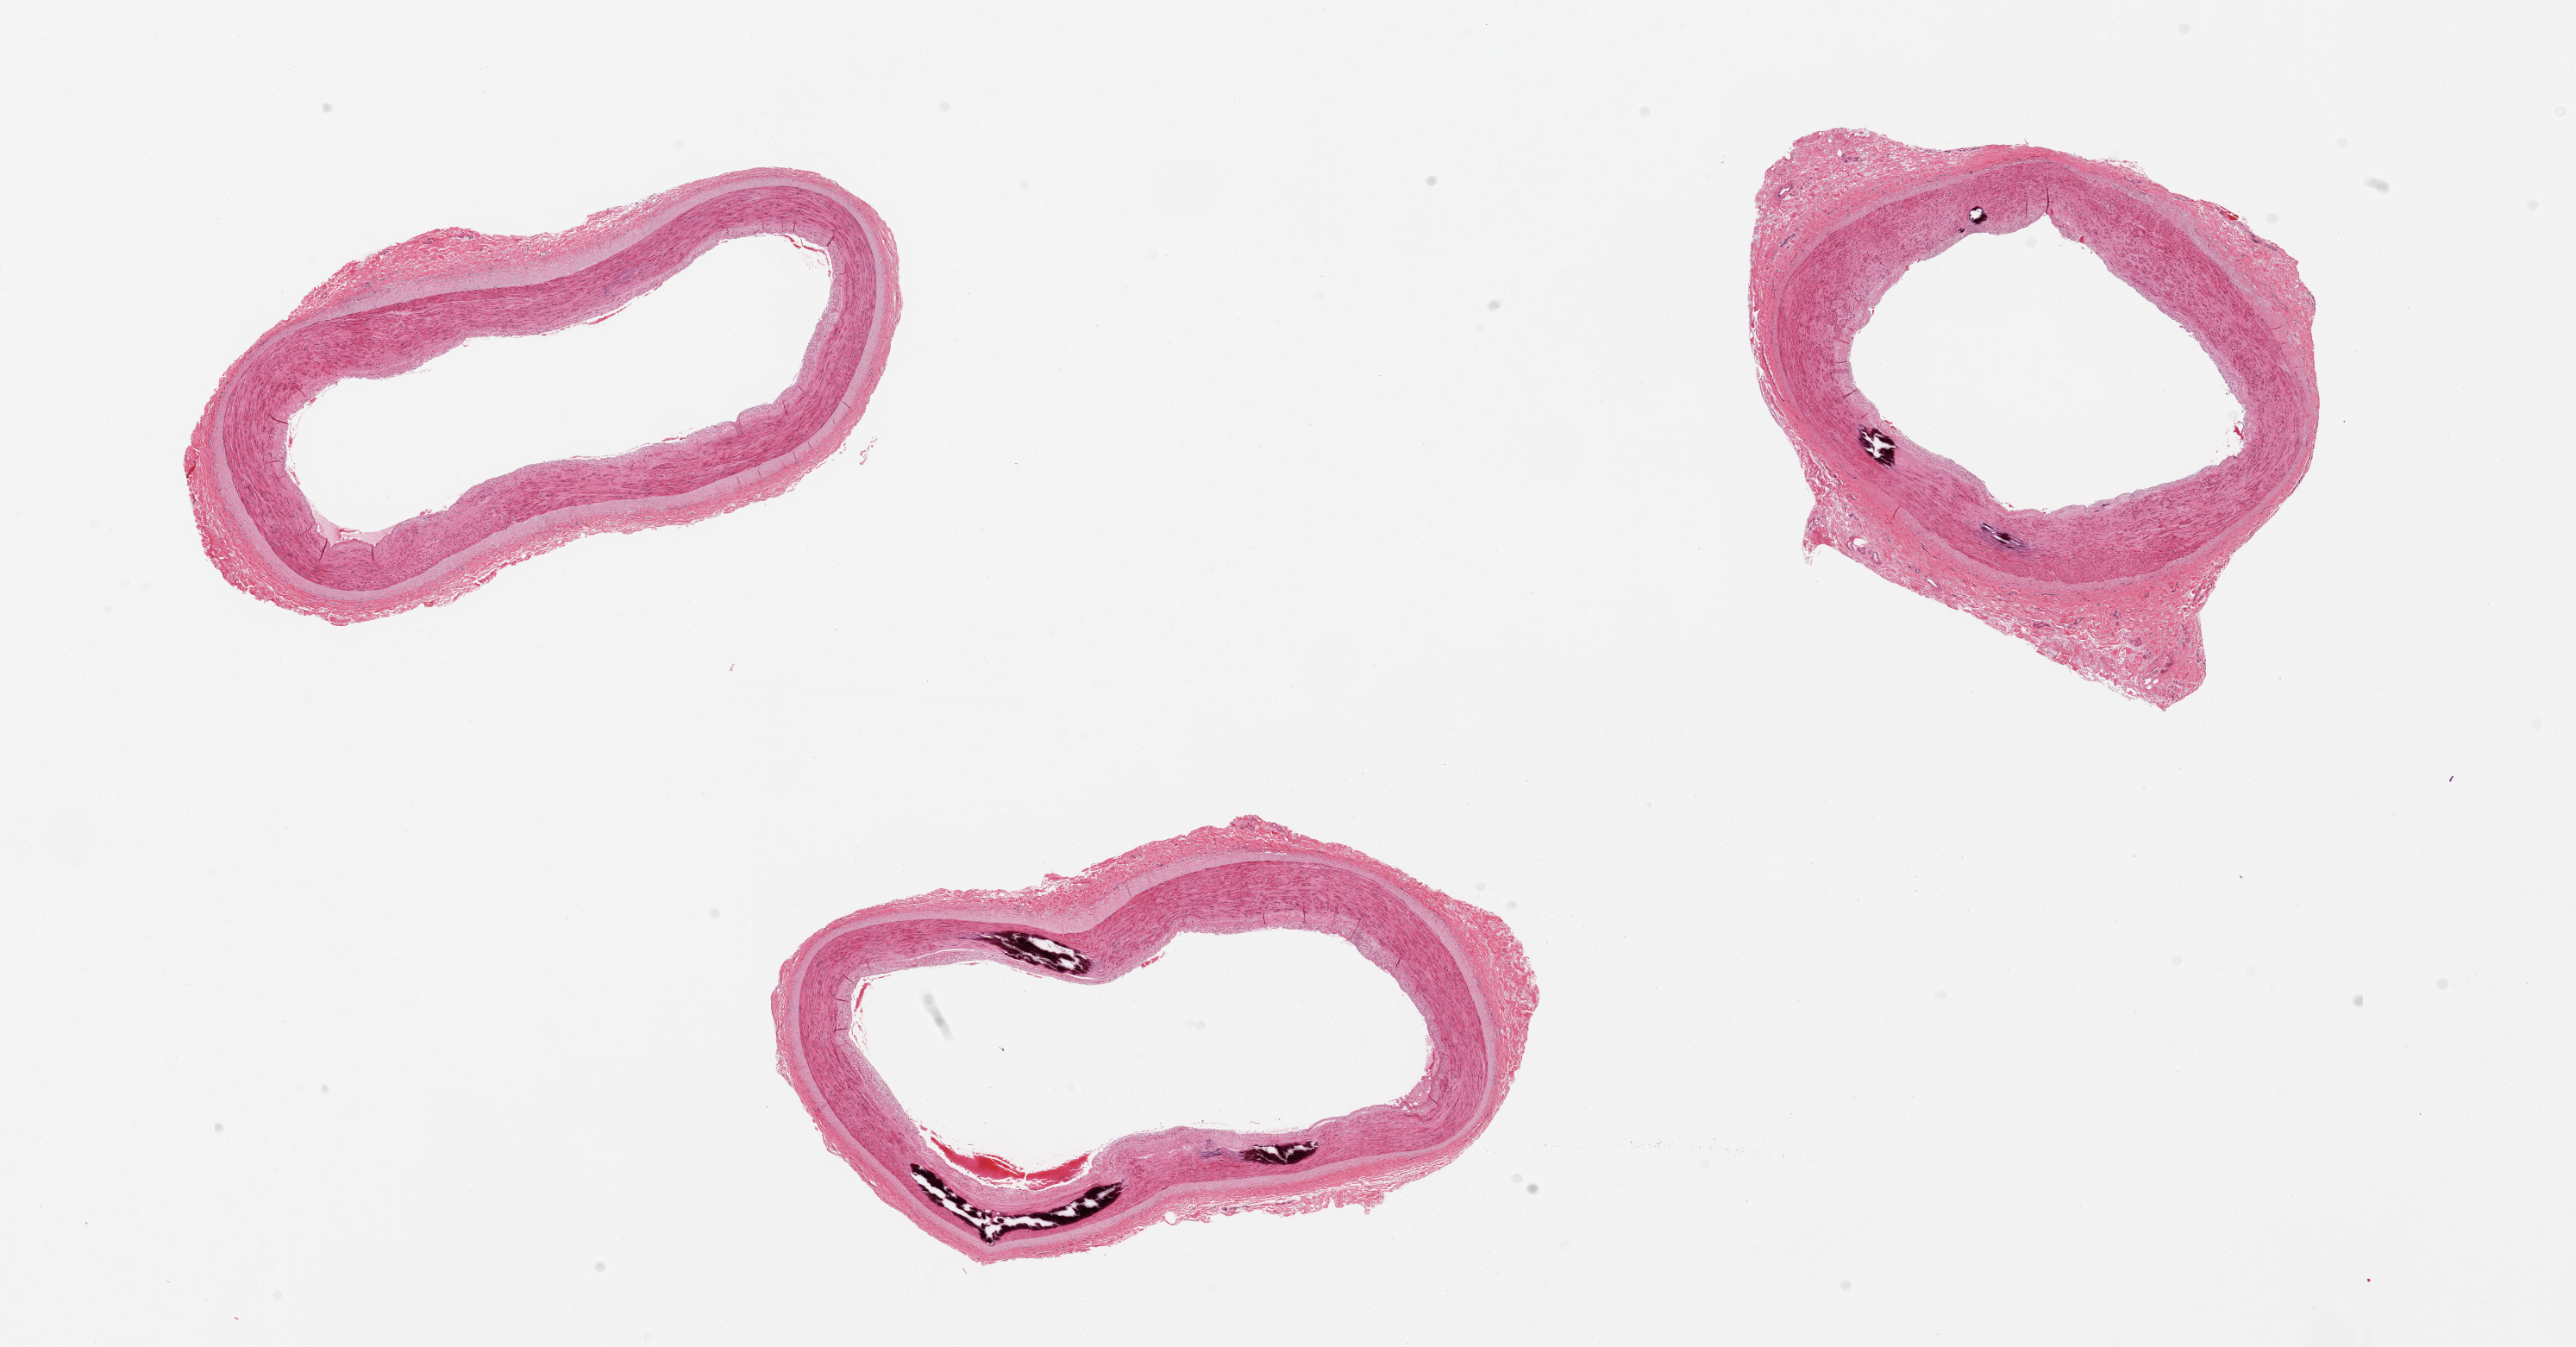
H&E whole-slide image, brightfield — whole scanned area (about 23.6 x 12.4 mm, acquisition: 20x scan) shown as a low-resolution overview, PAXgene-fixed paraffin-embedded (PFPE) section, target tissue: tibial artery, tissue donor sample. Donor: male.
• pathologist's review note for this sample: 3 pieces, generally clean sections; Monckebergs medial sclerosis